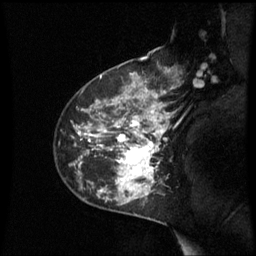
Breast MRI (dynamic contrast-enhanced), one sagittal slice. Slice 42 of 60 in the series (ordered by position). Dynamic contrast-enhanced series, image 2 of 3 at this slice position (ordered by acquisition). 1.5 T. TE 4.2 ms, TR 8.9 ms. 2.4 mm slice thickness. 256 × 256 image matrix. Patient: female, 42 years. Case-level facts recorded for this patient, not image findings: setting: breast cancer imaged before/during neoadjuvant chemotherapy; receptor status: HER2-positive.
Outlined on this slice (semi-automatically segmented with operator editing):
- analysis volume of interest (the breast-tissue region the enhancement analysis was run in; not a lesion): box from (x=64, y=93) to (x=171, y=210) px
- tumour enhancement mask (voxels above the 70 % enhancement threshold inside the analysis volume of interest): (x=79, y=93)–(x=170, y=193)